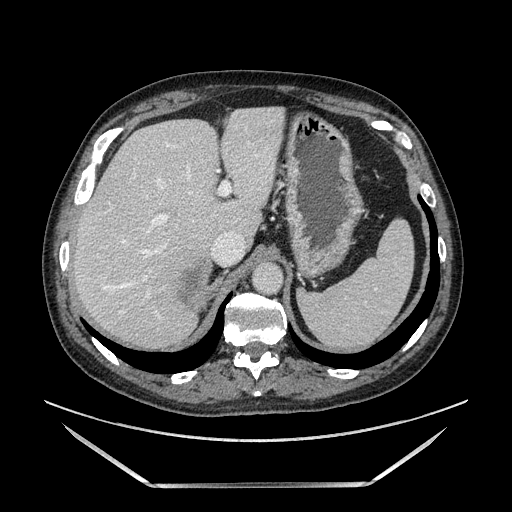
Contrast-enhanced abdominal CT, one axial slice. Slice 111 of 185 in the series (ordered by position). Soft-tissue window (W 400 / L 40 HU). 1.25 mm slice thickness. 512 × 512 image matrix. Male patient. From the clinical record (not read from this slice): diagnosis: adrenocortical carcinoma; tumour side: right adrenal; tumour size at pathology: 10.3 cm; Ki-67 index: 20 %; stage (as recorded): 3.
Annotated regions visible in this slice (semi-automatic segmentation, software-assisted and operator-edited):
- mass: box from (x=187, y=261) to (x=211, y=308) px